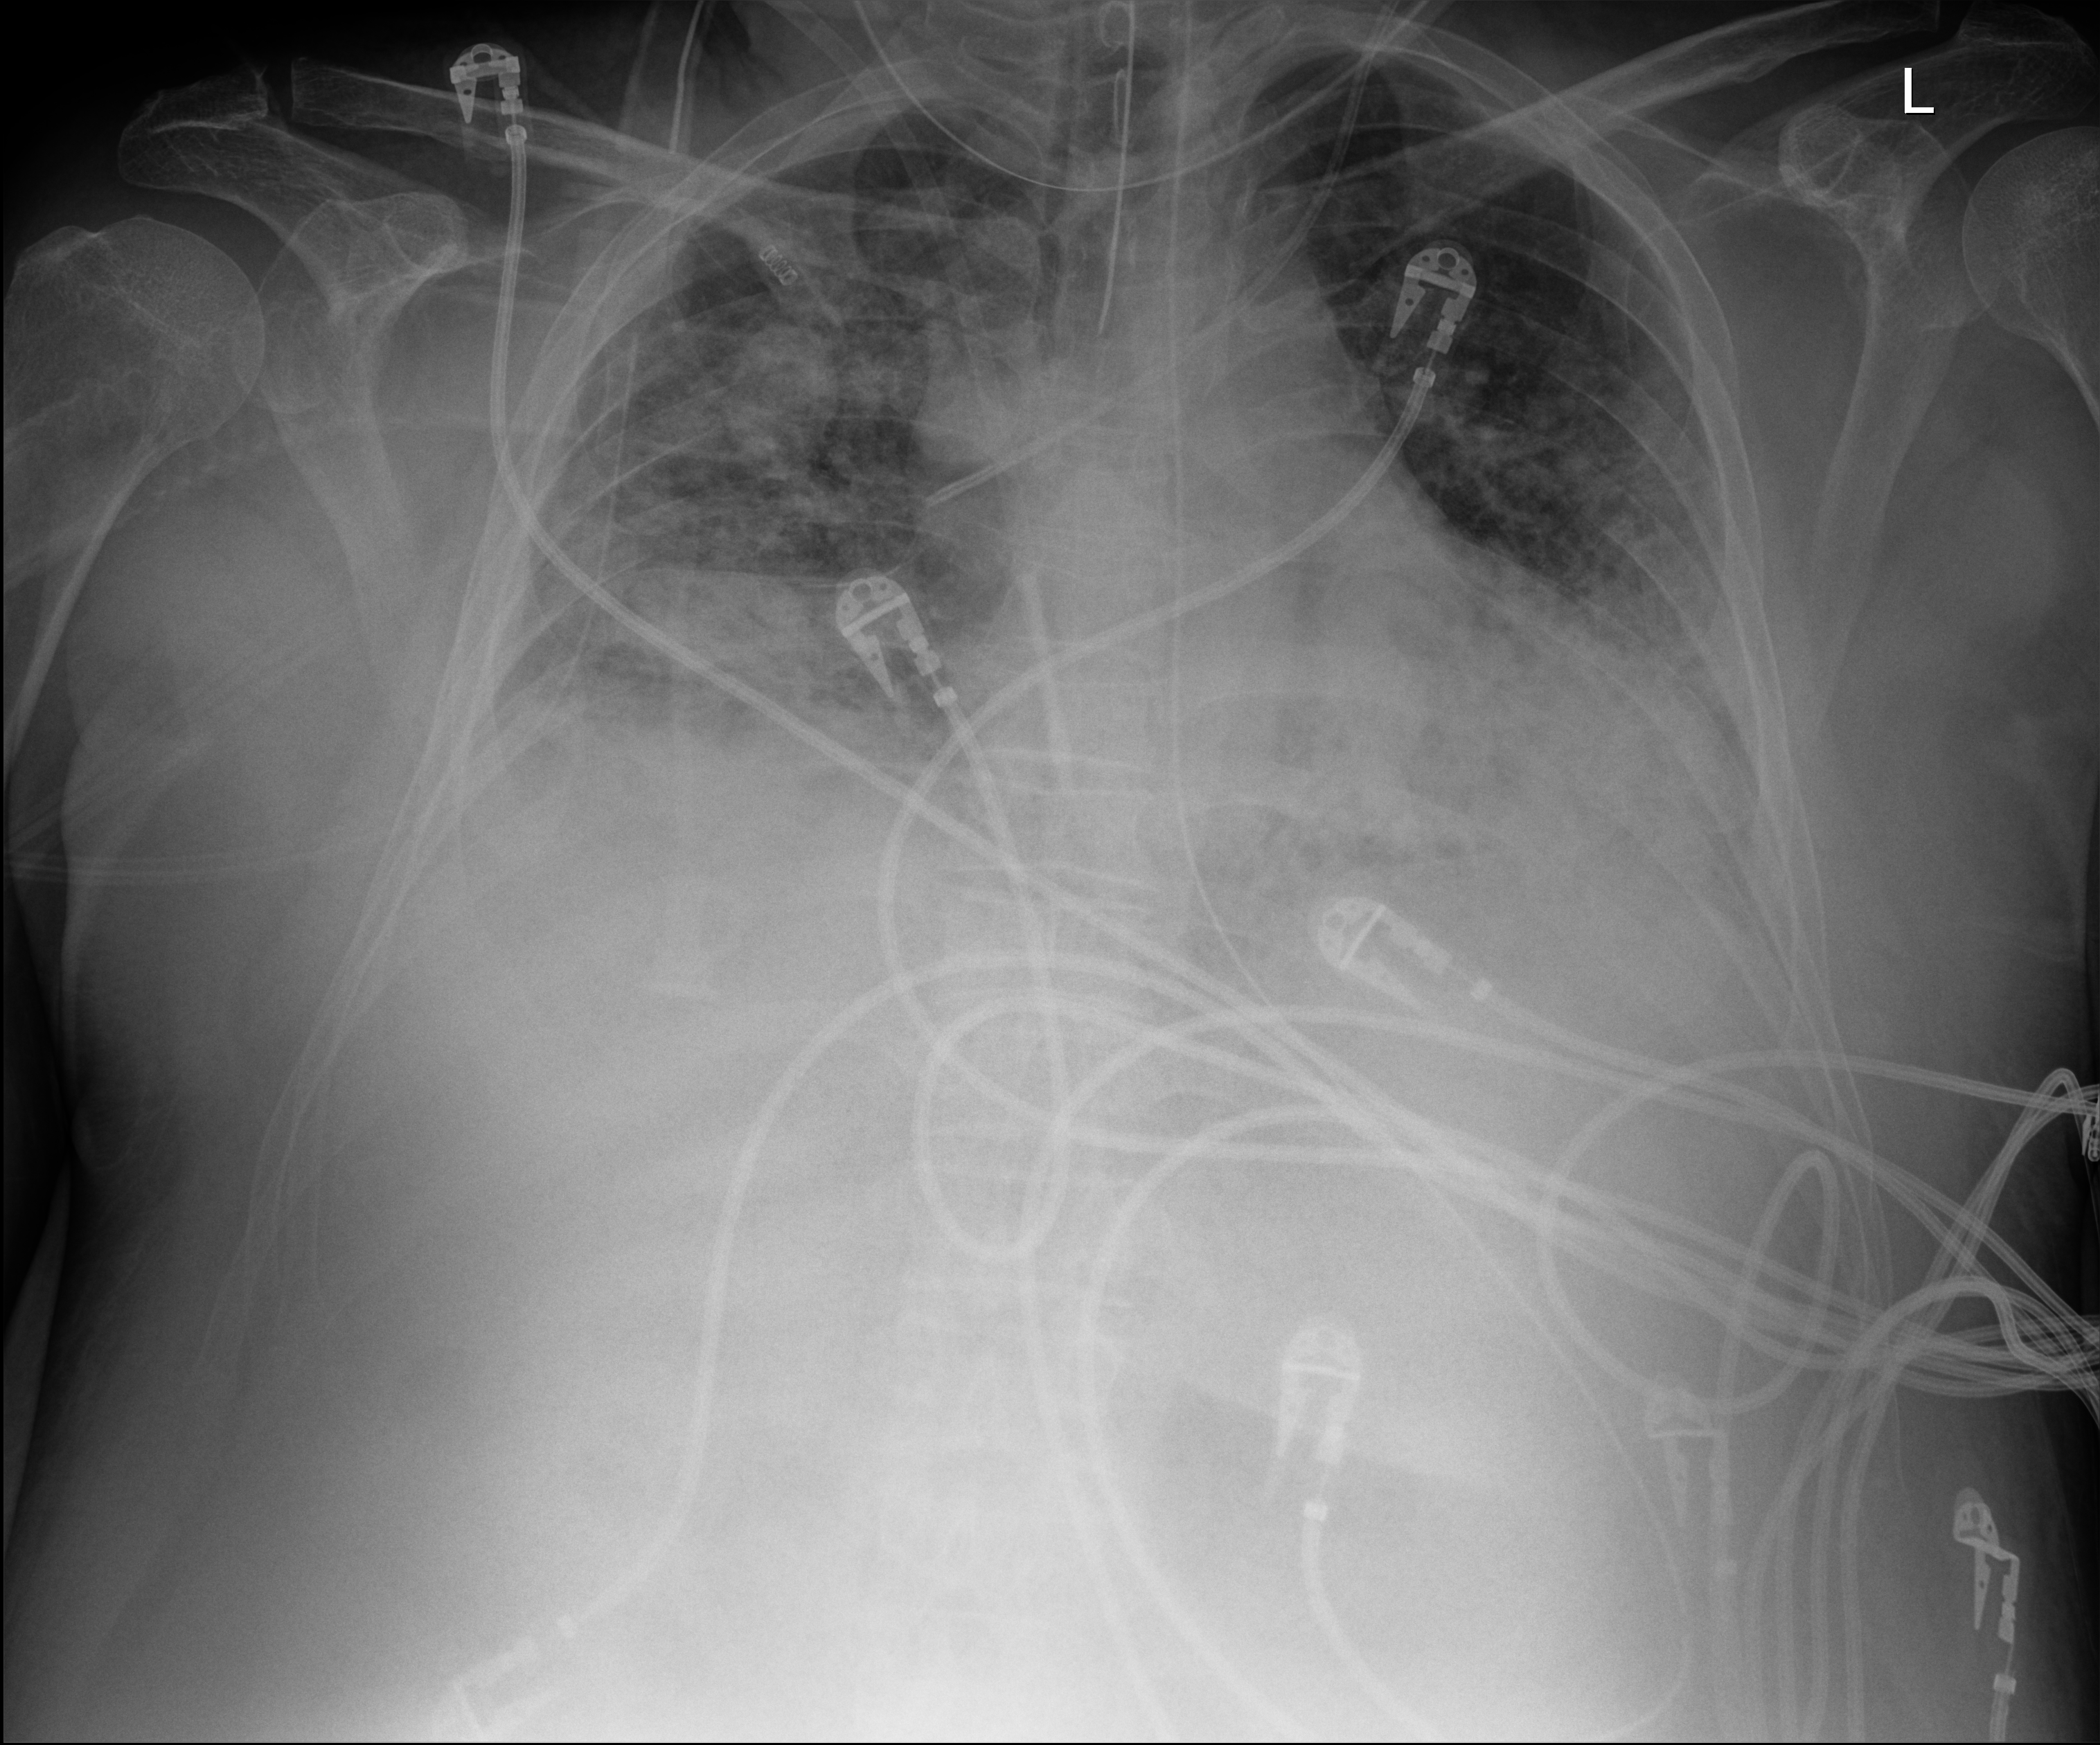
Bedside chest radiograph (digital radiography), anteroposterior (AP) projection. Patient hospitalised with COVID-19; male, aged 60–74 years.
Hospital-stay facts (about this admission, not read from this image; timing relative to this image not recorded):
- admitted to intensive care during this hospital stay: yes